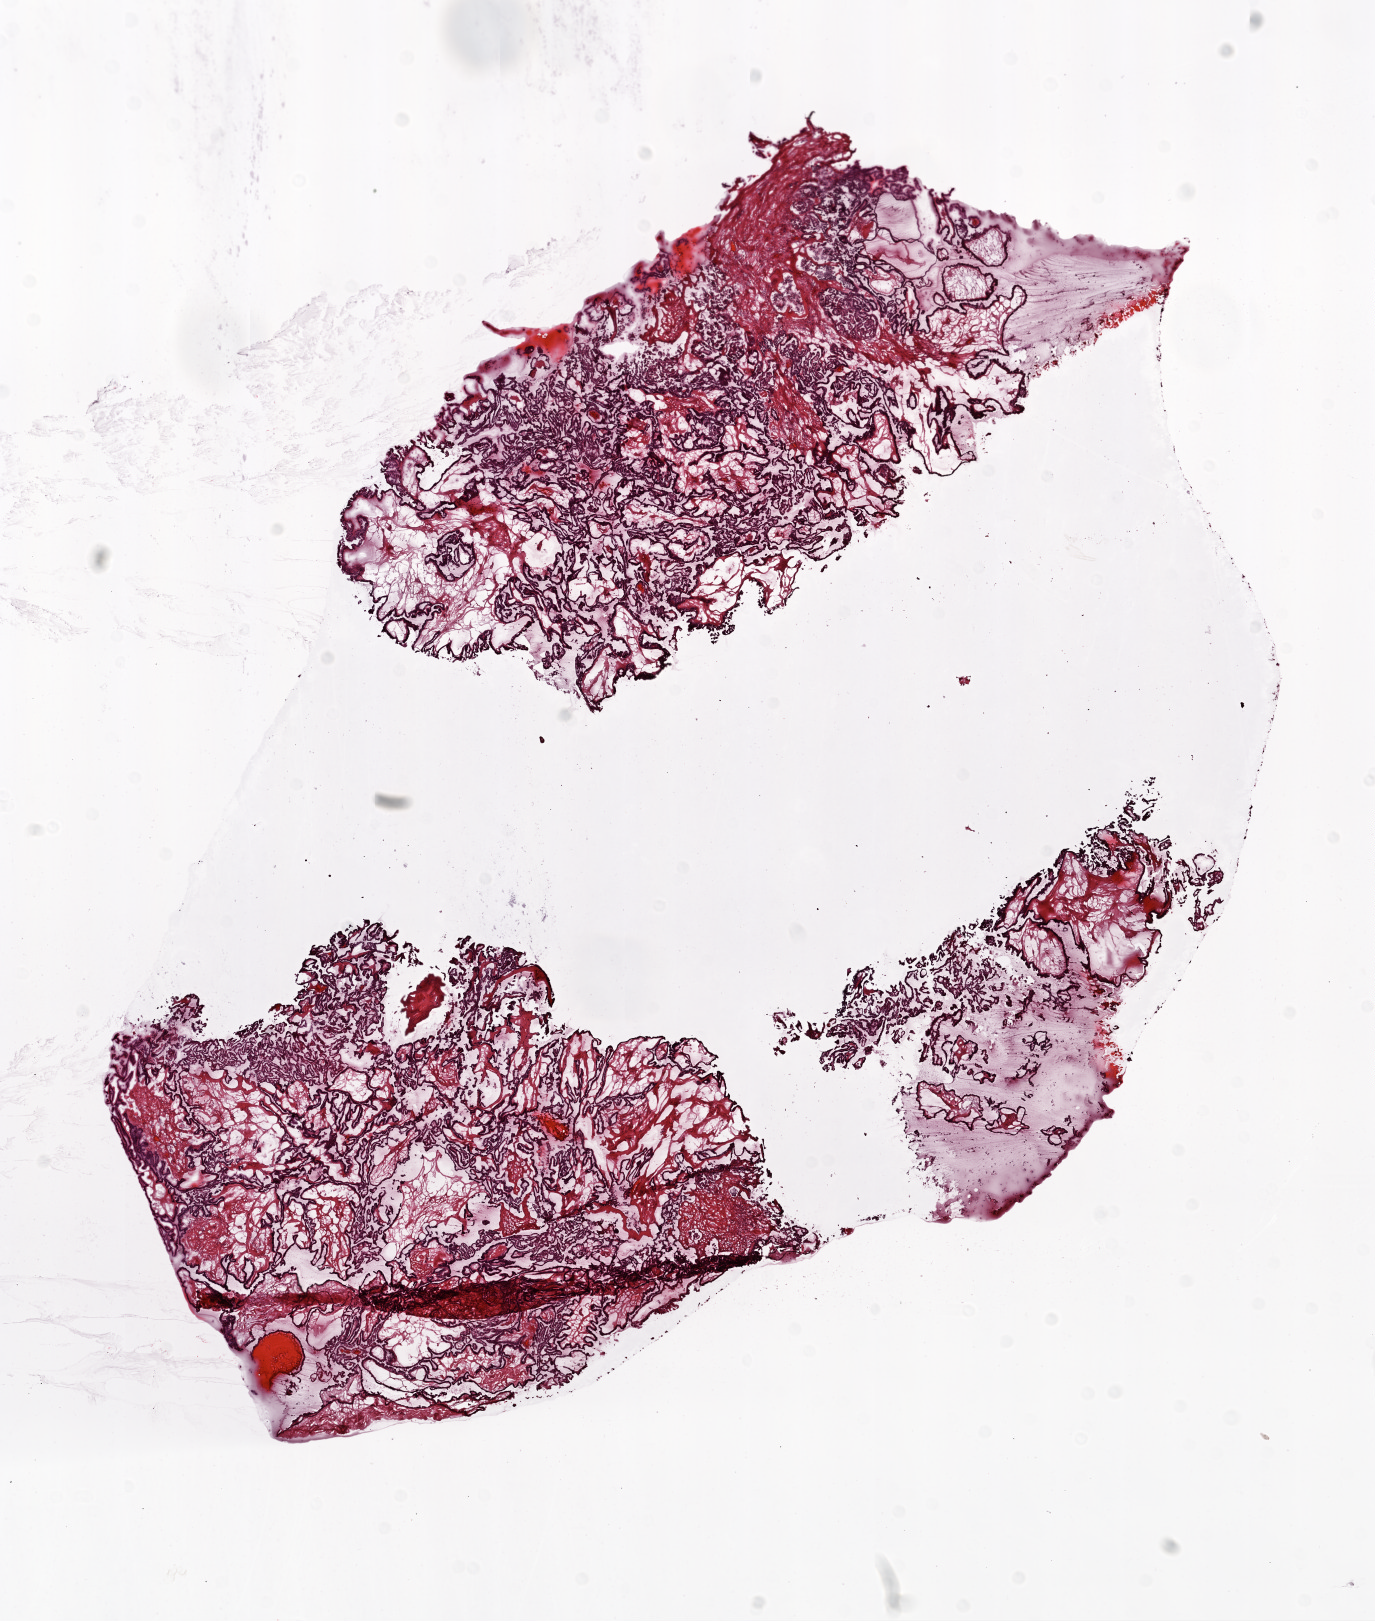
H&E-stained whole-slide image, a low-resolution overview of the entire scanned area, about 11.0 x 13.0 mm, frozen section, primary tumour sample from the ovary. Female, age 68 years at initial diagnosis. Histologic grade: GB (borderline). Slide review estimates, as recorded: tumour cells 95%, tumour nuclei 90%, normal cells 0%, stromal cells 5%, necrosis 0%. Inflammatory infiltration, as recorded: lymphocyte infiltration 0%, monocyte infiltration 0%, neutrophil infiltration 0%.
* histologic diagnosis: Serous cystadenocarcinoma, NOS
* FIGO stage: IIIA